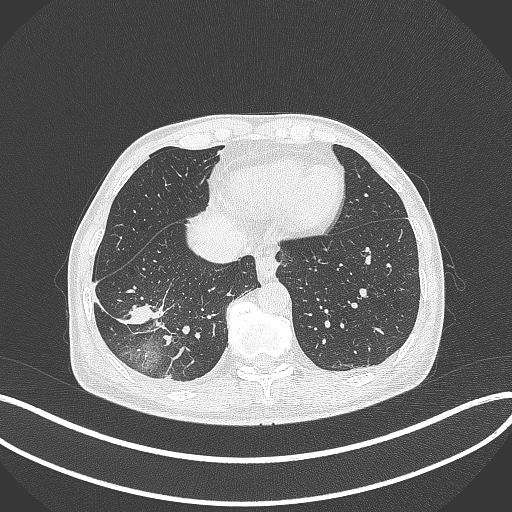
Chest CT, one axial slice; position 97 of 388 along the scan axis; reconstruction kernel B70f; 120 kVp; lung window (W 1500 / L -600 HU); 1 mm slice thickness; 512 × 512 image matrix, field of view 400 × 400 mm. Male patient, age 64 years. Case-level facts recorded for this patient, not image findings: clinical TNM (as recorded): T3 N0 M0.
Outlined on this slice (rectangle marked by the reading radiologist):
- lung tumour (recorded histology: adenocarcinoma): bounding box (x1, y1, x2, y2) in pixels: (114, 297, 166, 330)